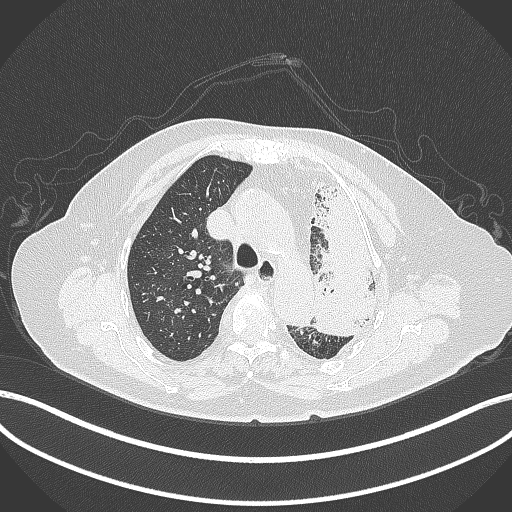
Chest CT, one axial slice; position 288 of 399 along the scan axis; reconstruction kernel B70f; 120 kVp; lung window (W 1500 / L -600 HU); 1 mm slice thickness; 512 × 512 image matrix, field of view 400 × 400 mm. Female patient, age 75 years. From the clinical record (not read from this slice): clinical TNM (as recorded): T3 N3 M1.
Outlined on this slice (rectangle marked by the reading radiologist):
- lung tumour (recorded histology: adenocarcinoma): box from (x=310, y=182) to (x=383, y=336) px